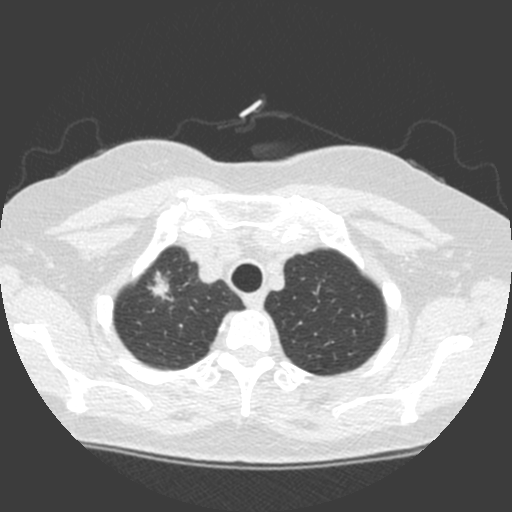
Low-dose screening chest CT, one axial slice. 120 kVp. Lung window (W 1500 / L -600 HU). 512 × 512 image matrix, field of view 314 × 314 mm.
Annotated regions visible in this slice (expert manual segmentation):
- lesion 1 (tumor, upper lobe of right lung): box from (x=147, y=271) to (x=173, y=301) px